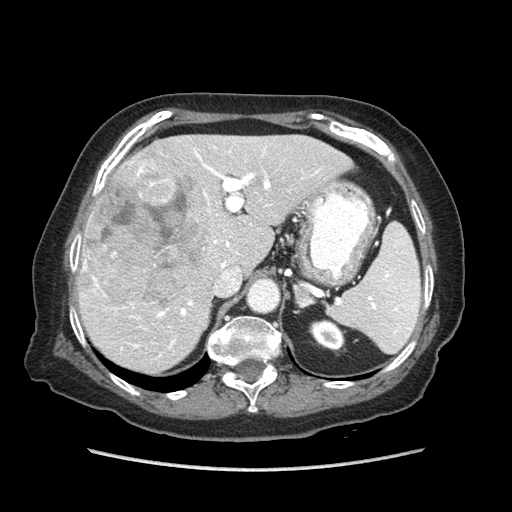
Contrast-enhanced abdominal CT (liver protocol), one axial slice; position 54 of 89 along the scan axis; reconstruction kernel STANDARD; 140 kVp; soft-tissue window (W 400 / L 40 HU); 512 × 512 image matrix, field of view 360 × 360 mm. From the clinical record (not read from this slice): diagnosis: hepatocellular carcinoma (patient treated with transarterial chemoembolisation; whether this scan precedes or follows treatment is not stated here); TNM stage (as recorded): Stage-IIIA; Child-Pugh class: A; tumour differentiation: well differentiated; tumour nodularity: multinodular.
Annotated regions visible in this slice (semi-automatically segmented with operator editing):
- liver parenchyma outside the tumour (the mass and vessels are separate outlines, so this box may not span the whole liver): bounding box [x1, y1, x2, y2] px = [78, 134, 352, 372]
- mass: [85, 155, 208, 305]
- liver vessels: [83, 147, 319, 357]